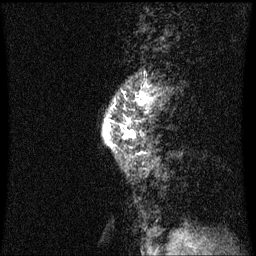
Breast MRI (dynamic contrast-enhanced), one sagittal slice; slice 19 of 60 in the series (ordered by position); dynamic contrast-enhanced series, image 2 of 3 at this slice position (ordered by acquisition); 1.5 T; TE 4.2 ms, TR 8.9 ms; 256 × 256 image matrix, field of view 200 × 200 mm. Female patient, age 50 years. Case-level facts recorded for this patient, not image findings: setting: breast cancer imaged before/during neoadjuvant chemotherapy; receptor status: triple-negative.
Outlined on this slice (semi-automatic segmentation, software-assisted and operator-edited):
- analysis volume of interest (the breast-tissue region the enhancement analysis was run in; not a lesion): bounding box <104,84,157,161> (left, top, right, bottom; pixels)
- tumour enhancement mask (voxels above the 70 % enhancement threshold inside the analysis volume of interest): <122,96,153,139>